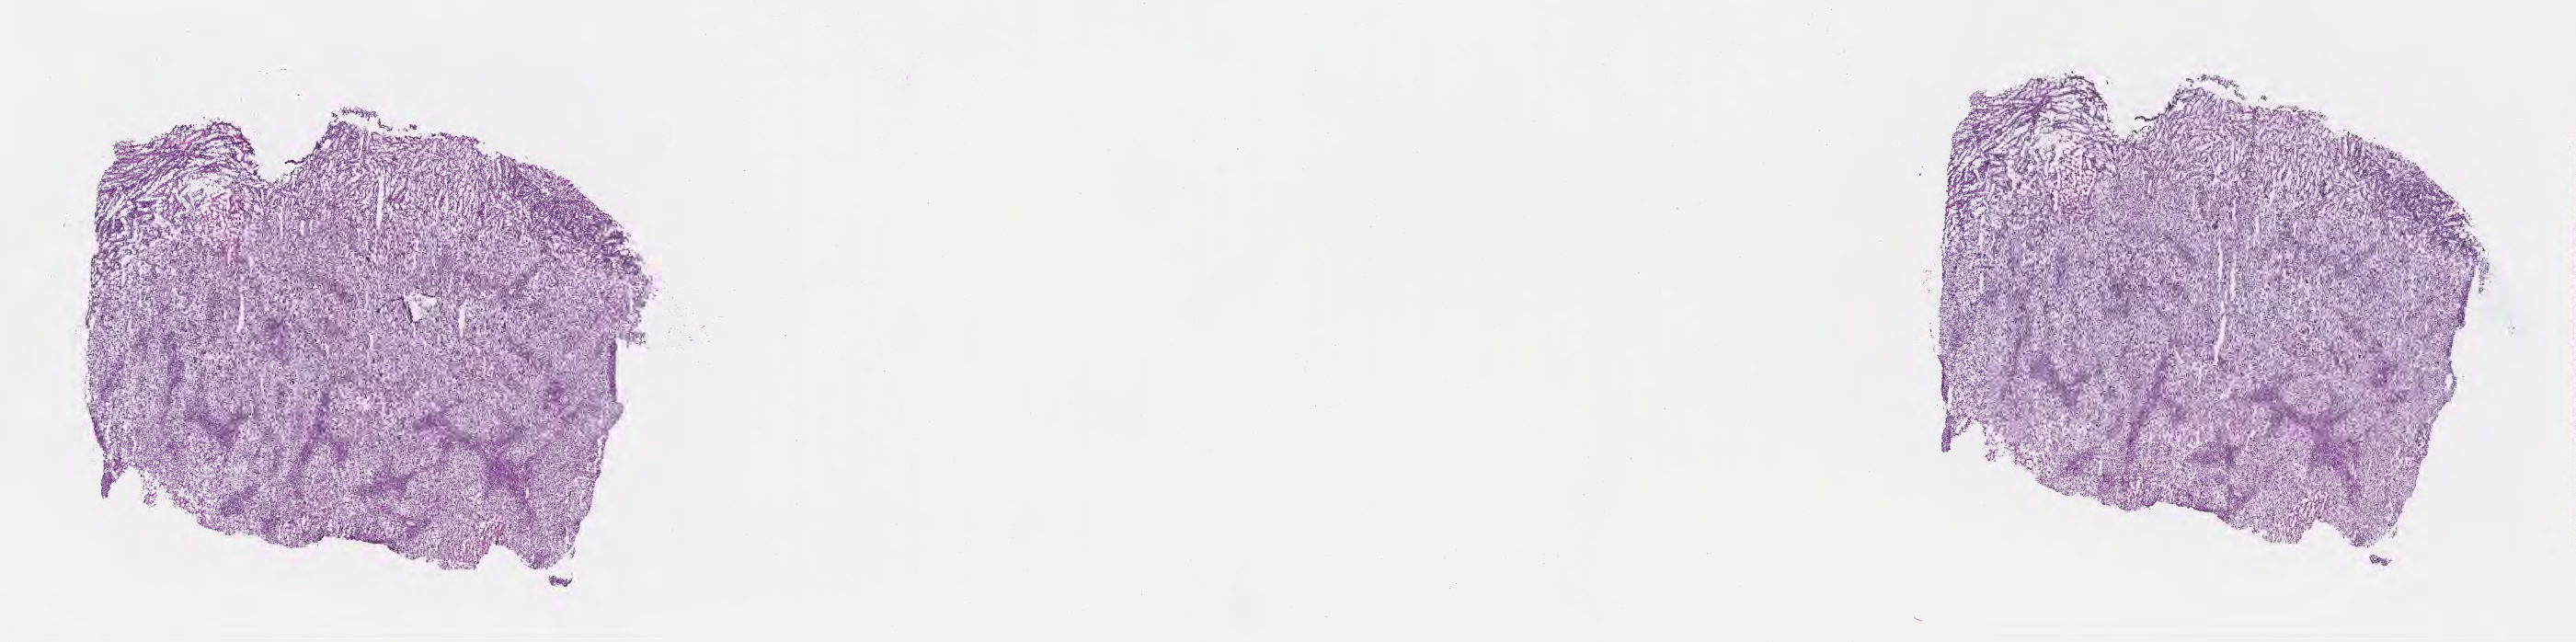
Hematoxylin and eosin (H&E) whole-slide image, a low-resolution overview of the entire scanned area, about 22.6 x 5.6 mm; frozen section (tissue freezing medium); specimen: metastatic tumor tissue, resected from lymph node. Male, age 53 years at initial diagnosis. Composition of this section per pathologist review: tumor cells 20%, tumor nuclei 65%, stromal cells 77%, necrosis 3%, normal cells 0%. Infiltration values recorded for this section: lymphocyte infiltration 28%, monocyte infiltration 2%, neutrophil infiltration 0%.
• patient diagnosis (primary): Malignant melanoma, NOS
• section: bottom of the tissue portion